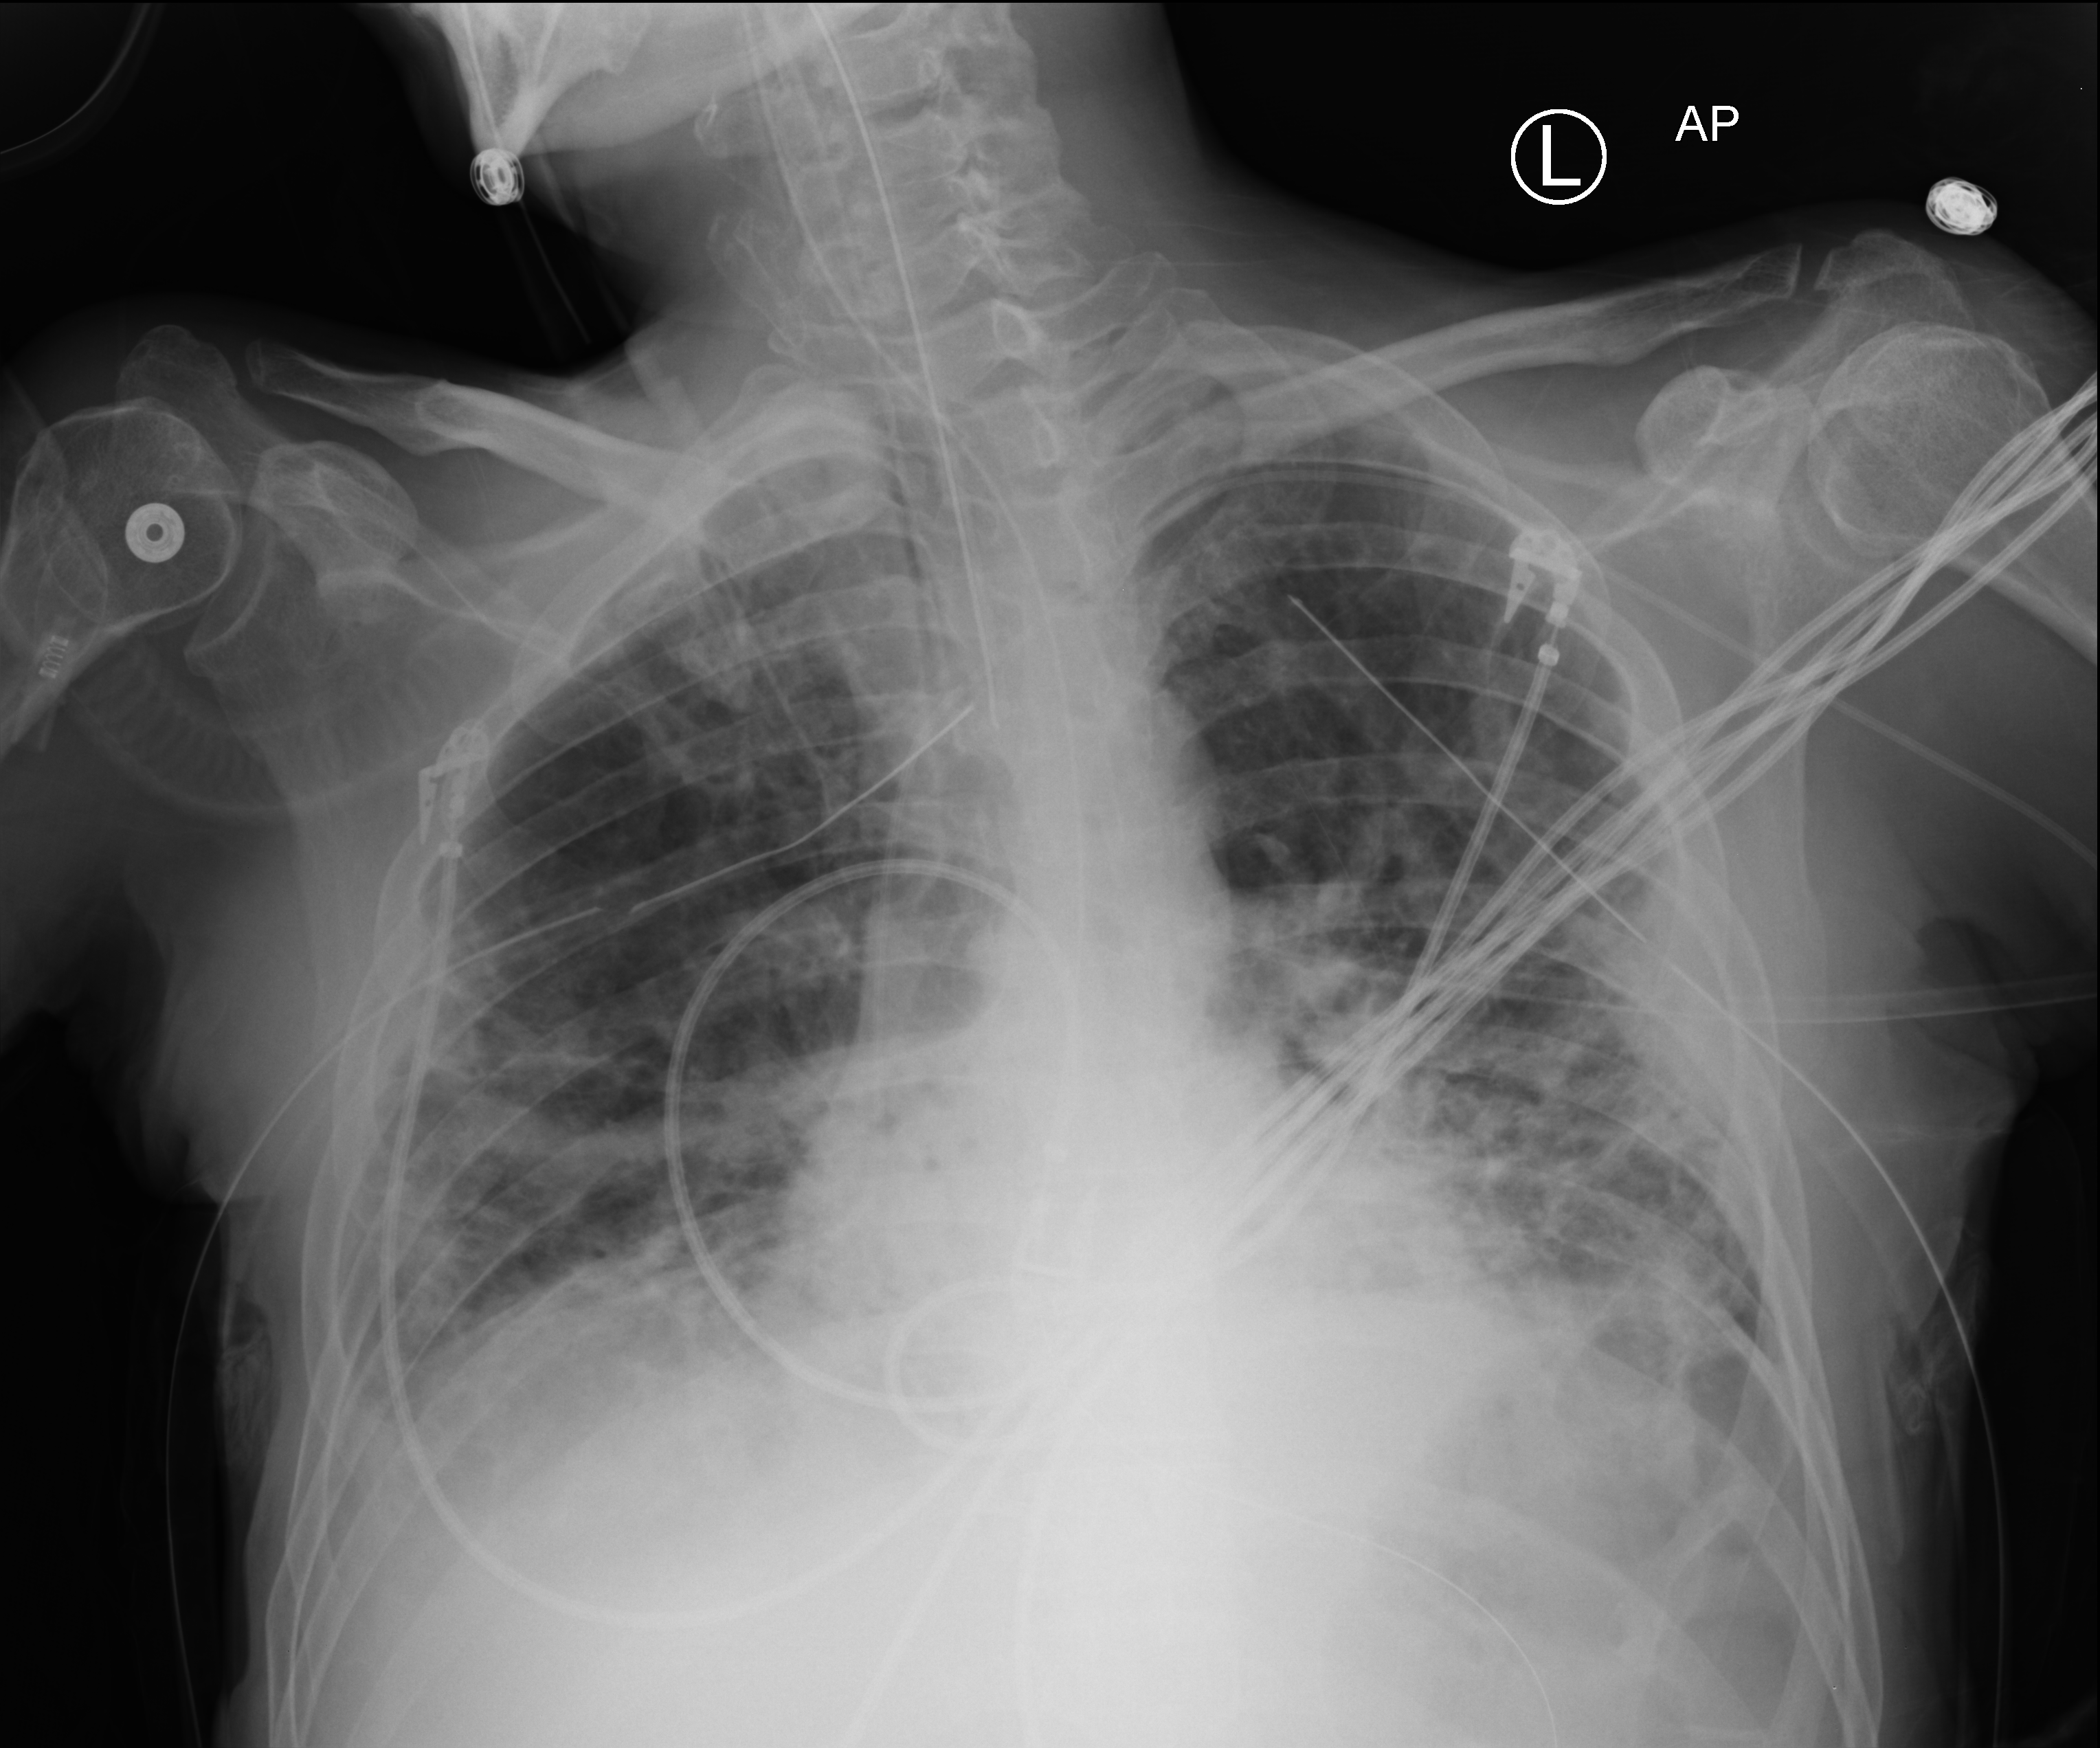
Chest X-ray (portable). Patient hospitalised with COVID-19; male, aged 18–59 years.
Hospital-stay facts (about this admission, not read from this image; timing relative to this image not recorded):
- admitted to intensive care during this hospital stay: yes